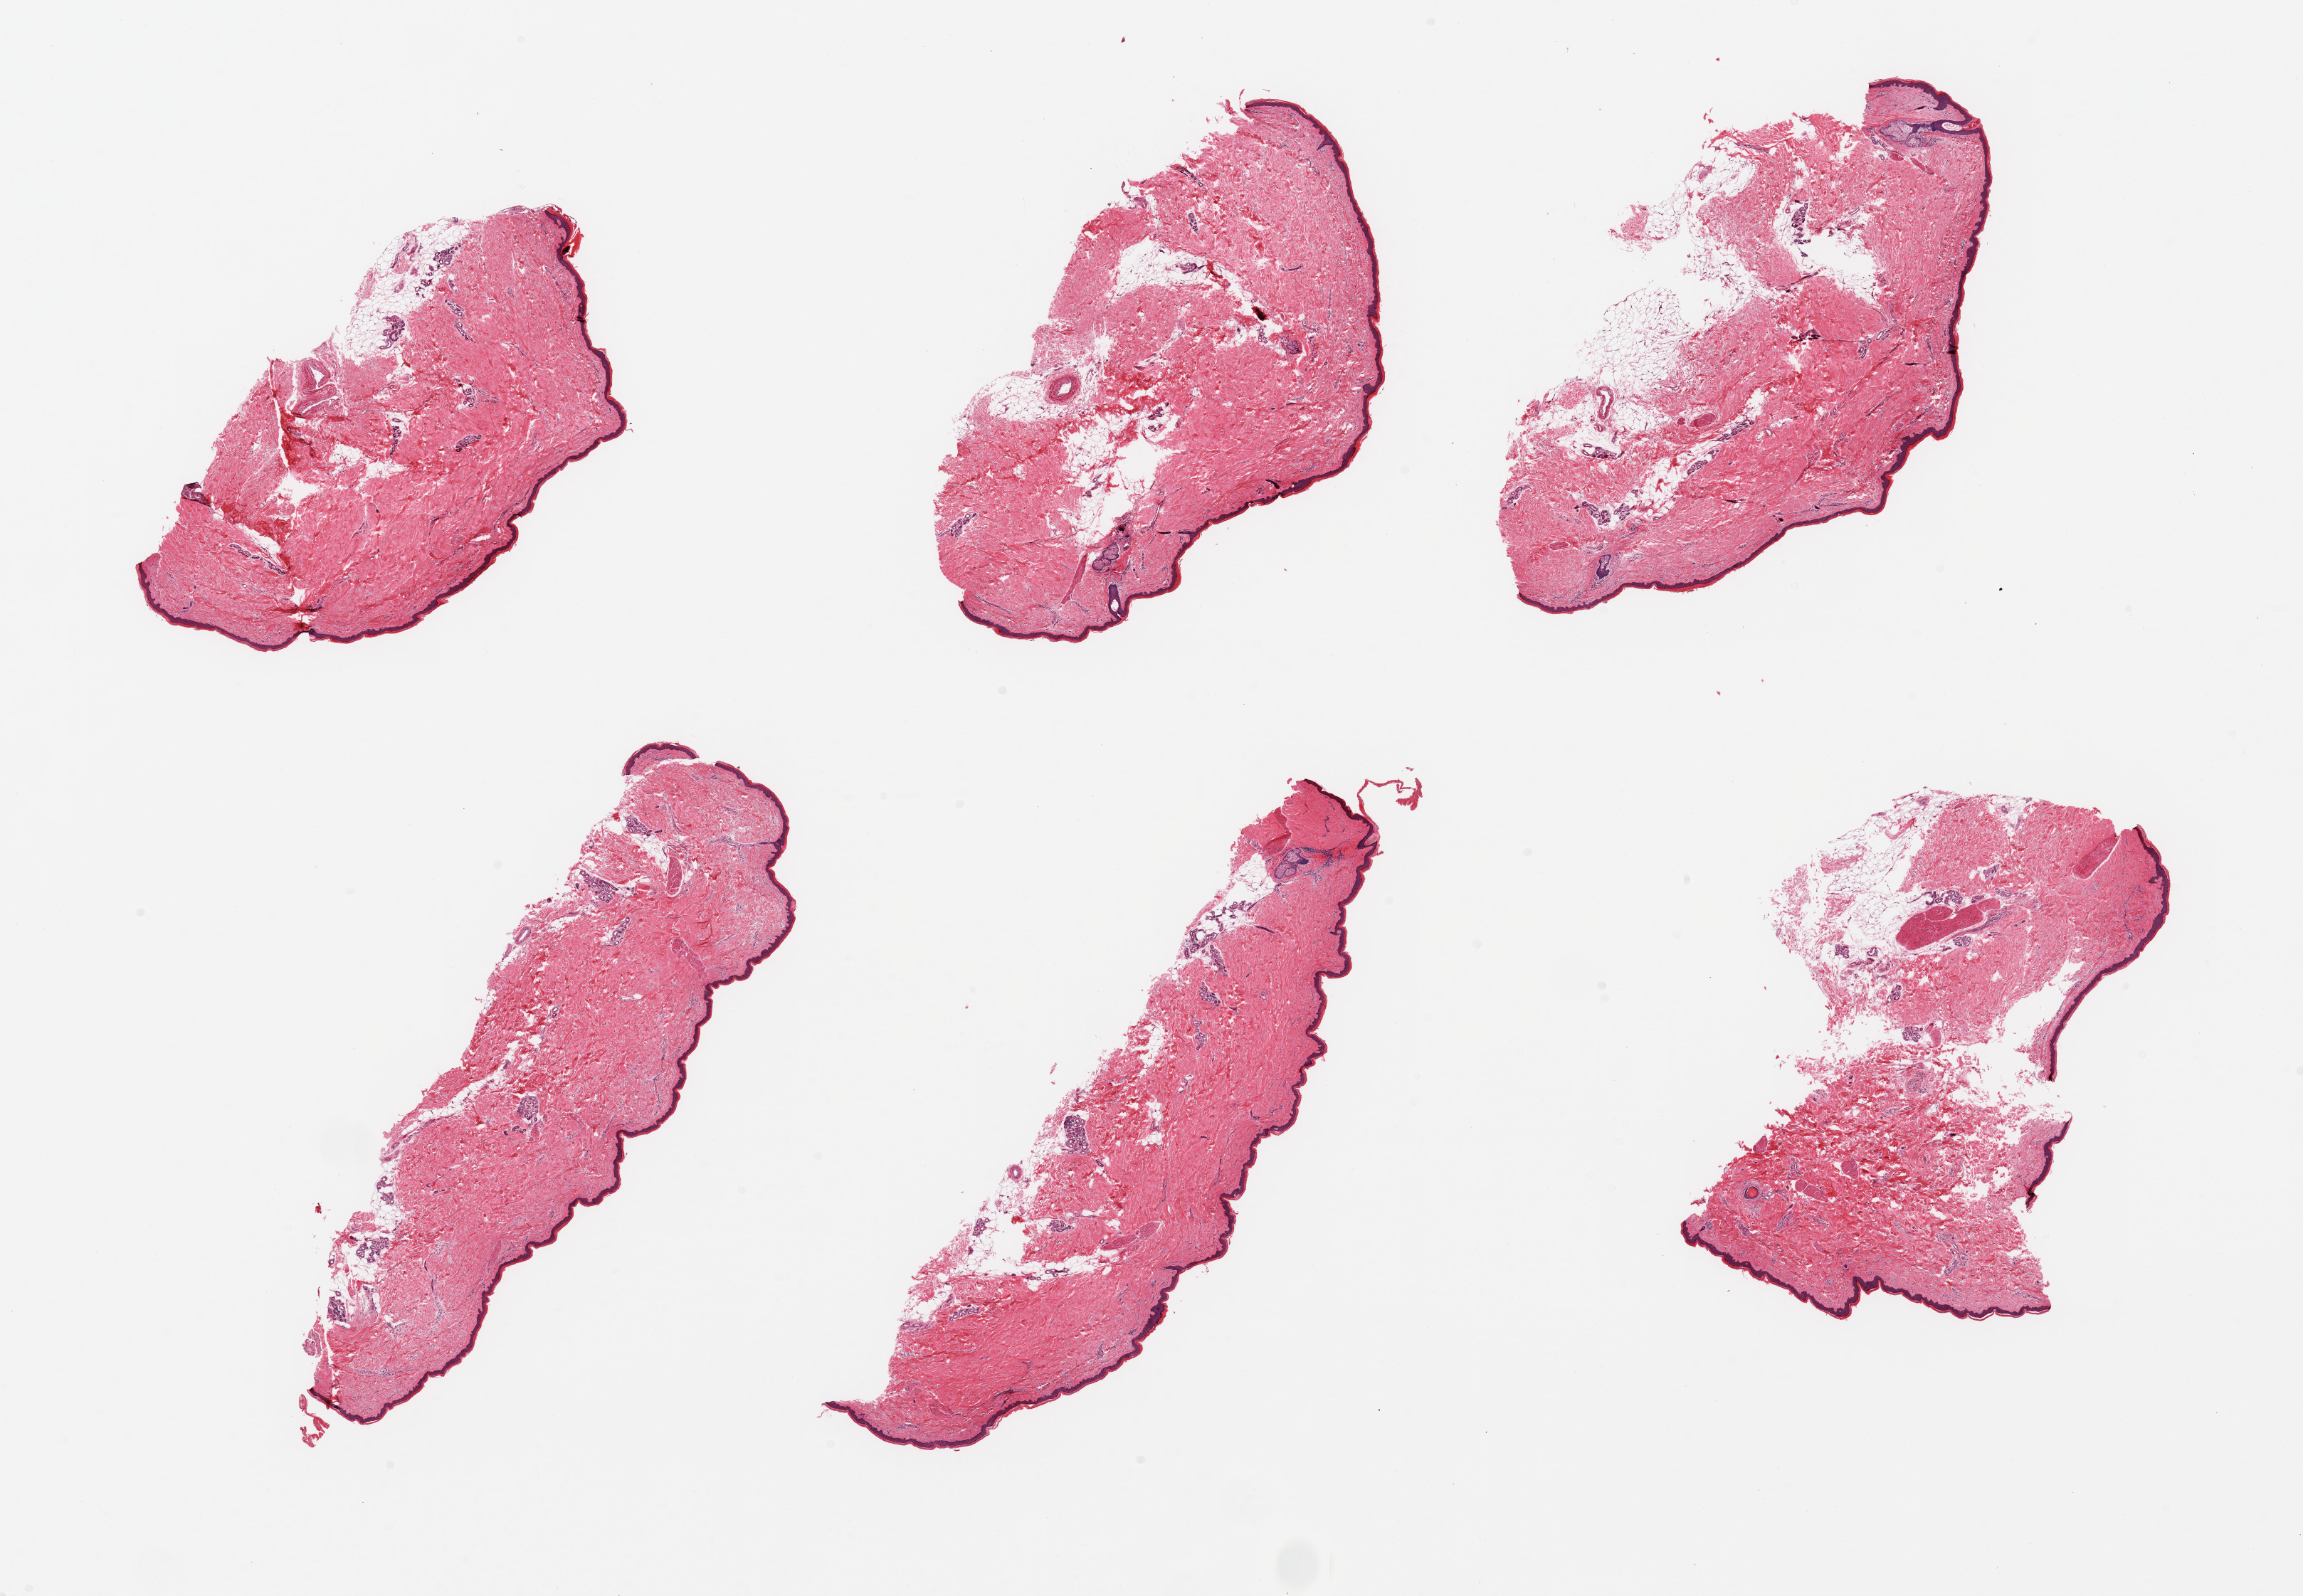
Haematoxylin and eosin whole-slide image, low-resolution overview of the scanned area, about 25.6 x 17.7 mm. PAXgene-fixed paraffin-embedded (PFPE) section. Target tissue: skin of lower leg. Donor tissue sample. Female donor.
• review note (as recorded): 6 pieces; up to 20% dermal fat